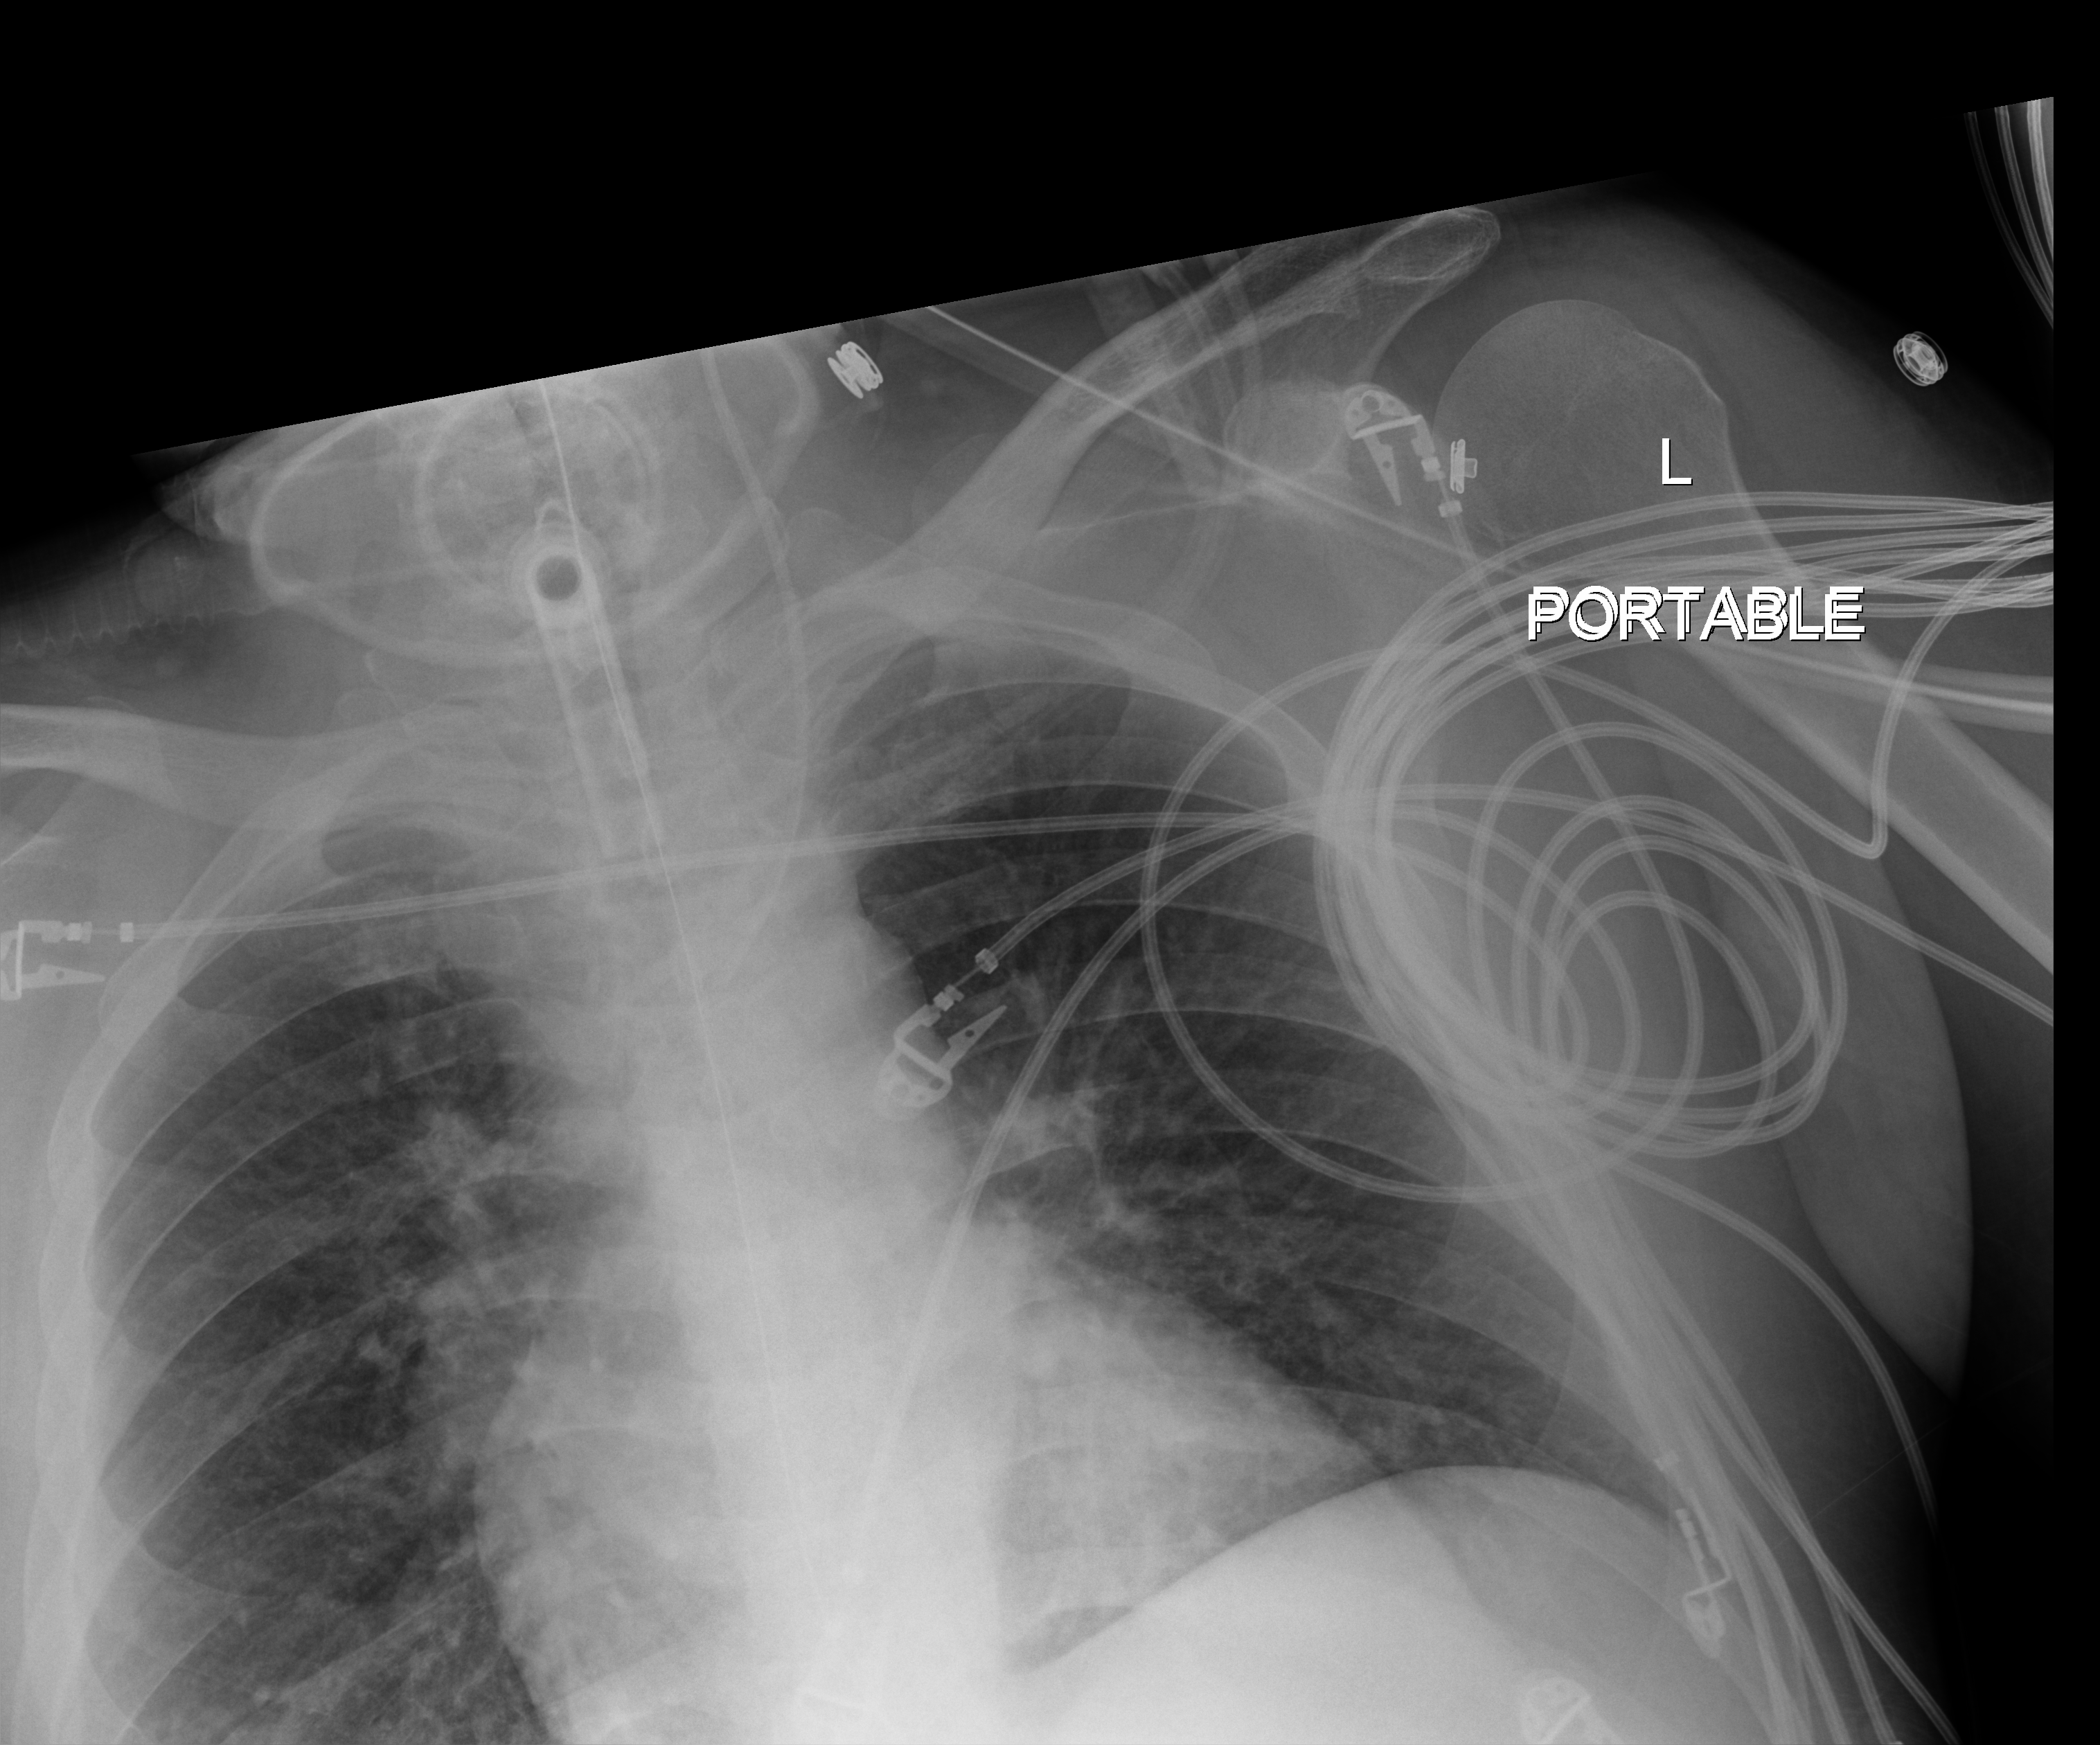
Chest X-ray (portable); anteroposterior (AP) projection. Patient hospitalised with COVID-19; female, aged 75–90 years.
Hospital-stay facts (about this admission, not read from this image; timing relative to this image not recorded): diabetes (admission record): no; length of hospital stay: 70 days; smoking status (admission record): former.